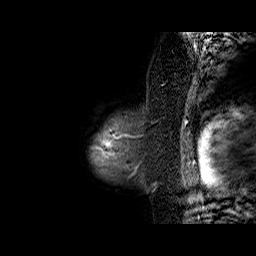
Breast MRI (dynamic contrast-enhanced), one sagittal slice. Slice 53 of 60 in the series (ordered by position). Dynamic contrast-enhanced series, time point 2 of 6 at this slice position (early post-contrast). 1.5 T. TE 6.3 ms, TR 32.4 ms. 4 mm slice thickness. 256 × 256 image matrix, field of view 200 × 200 mm. Female patient. From the clinical record (not read from this slice): setting: breast cancer imaged before/during neoadjuvant chemotherapy; receptor status: triple-negative.
Annotated regions visible in this slice (semi-automatic segmentation, software-assisted and operator-edited):
- analysis volume of interest (the breast-tissue region the enhancement analysis was run in; not a lesion): bounding box [x1, y1, x2, y2] px = [90, 95, 157, 187]
- tumour enhancement mask (voxels above the 100 % enhancement threshold inside the analysis volume of interest): [94, 129, 118, 158]